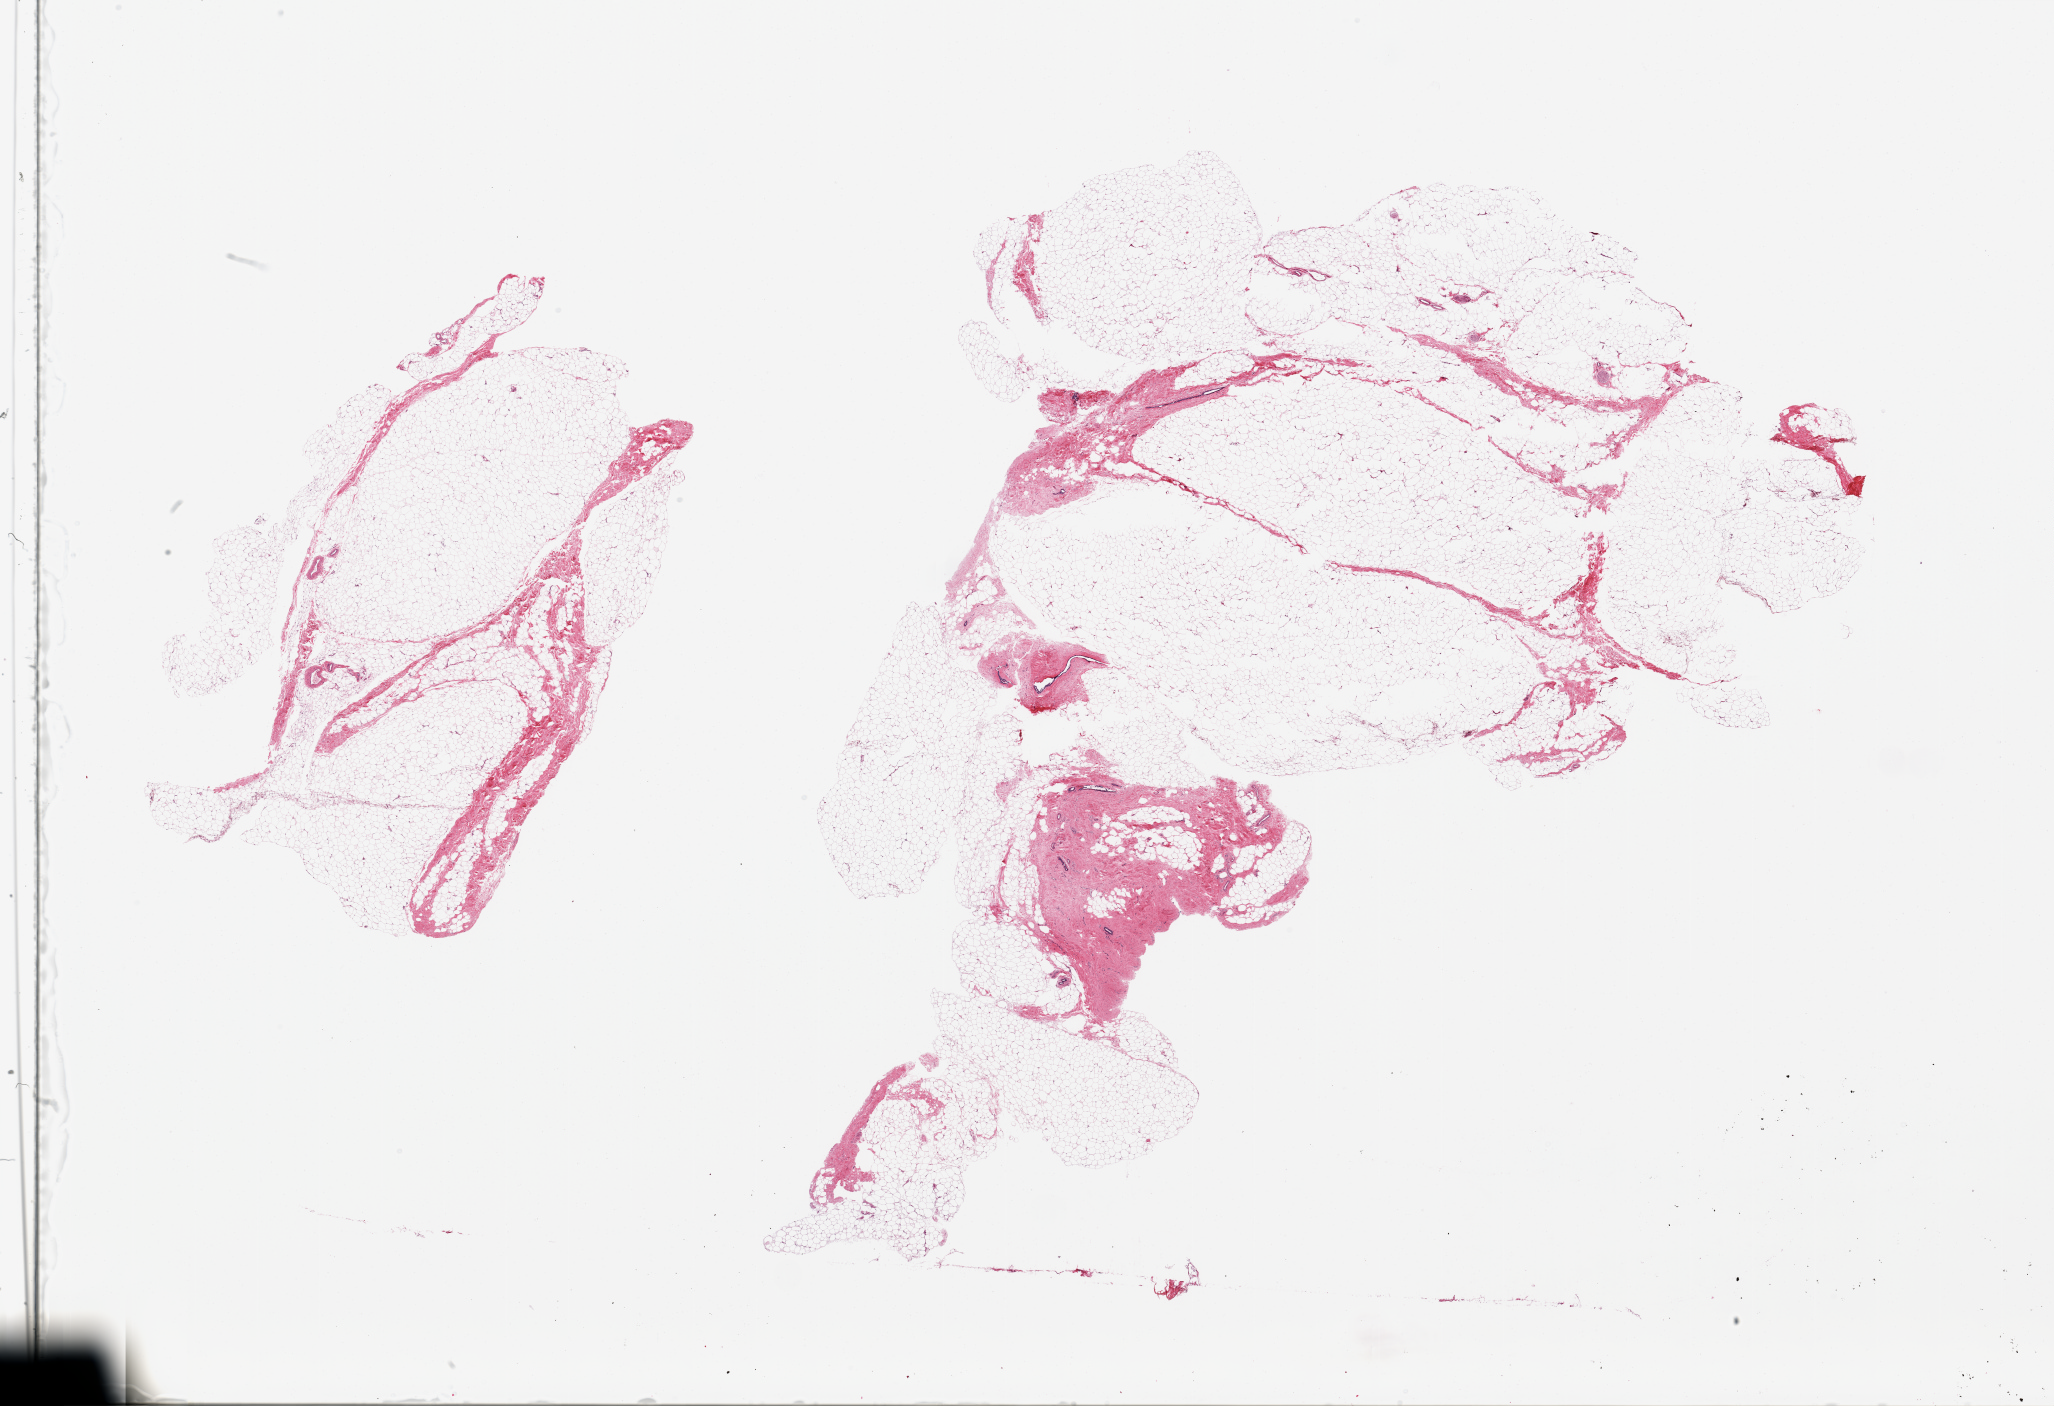
Whole-slide image, H&E stain, a low-resolution overview of the entire scanned area, about 32.5 x 22.2 mm (from a 20x scan); PAXgene-fixed paraffin-embedded (PFPE) section; section of breast (target tissue); tissue donor sample. Donor sex: male.
Review note (as recorded): 2 pieces; occasional ducts.